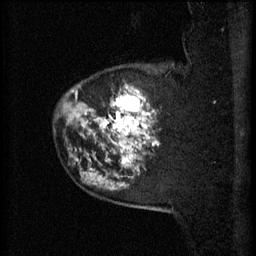
Breast MRI (dynamic contrast-enhanced), one sagittal slice. 3 images stored at this slice position (order not interpretable as contrast timing). 1.5 T. TE 4.2 ms, TR 11 ms. 256 × 256 image matrix, field of view 180 × 180 mm. Patient: female, 52 years.
Structures marked on this image (semi-automatically segmented with operator editing):
- analysis volume of interest (the breast-tissue region the enhancement analysis was run in; not a lesion): box from (x=81, y=66) to (x=161, y=157) px
- tumour enhancement mask (voxels above the 70 % enhancement threshold inside the analysis volume of interest): (x=81, y=86)–(x=160, y=157)